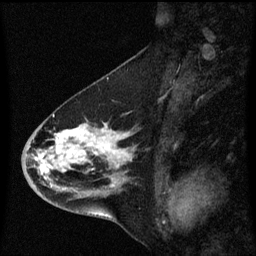
Breast MRI (dynamic contrast-enhanced), one sagittal slice. Slice 28 of 60 in the series (ordered by position). Dynamic contrast-enhanced series, image 2 of 3 at this slice position (ordered by acquisition). 1.5 T. TE 4.2 ms, TR 8.4 ms. 256 × 256 image matrix, field of view 200 × 200 mm. Patient: female, 46 years. Case-level facts recorded for this patient, not image findings: setting: breast cancer imaged before/during neoadjuvant chemotherapy; receptor status: HER2-positive.
Structures marked on this image (semi-automatic segmentation, software-assisted and operator-edited):
- analysis volume of interest (the breast-tissue region the enhancement analysis was run in; not a lesion): bounding box <22,112,136,195> (left, top, right, bottom; pixels)
- tumour enhancement mask (voxels above the 70 % enhancement threshold inside the analysis volume of interest): <38,124,131,187>